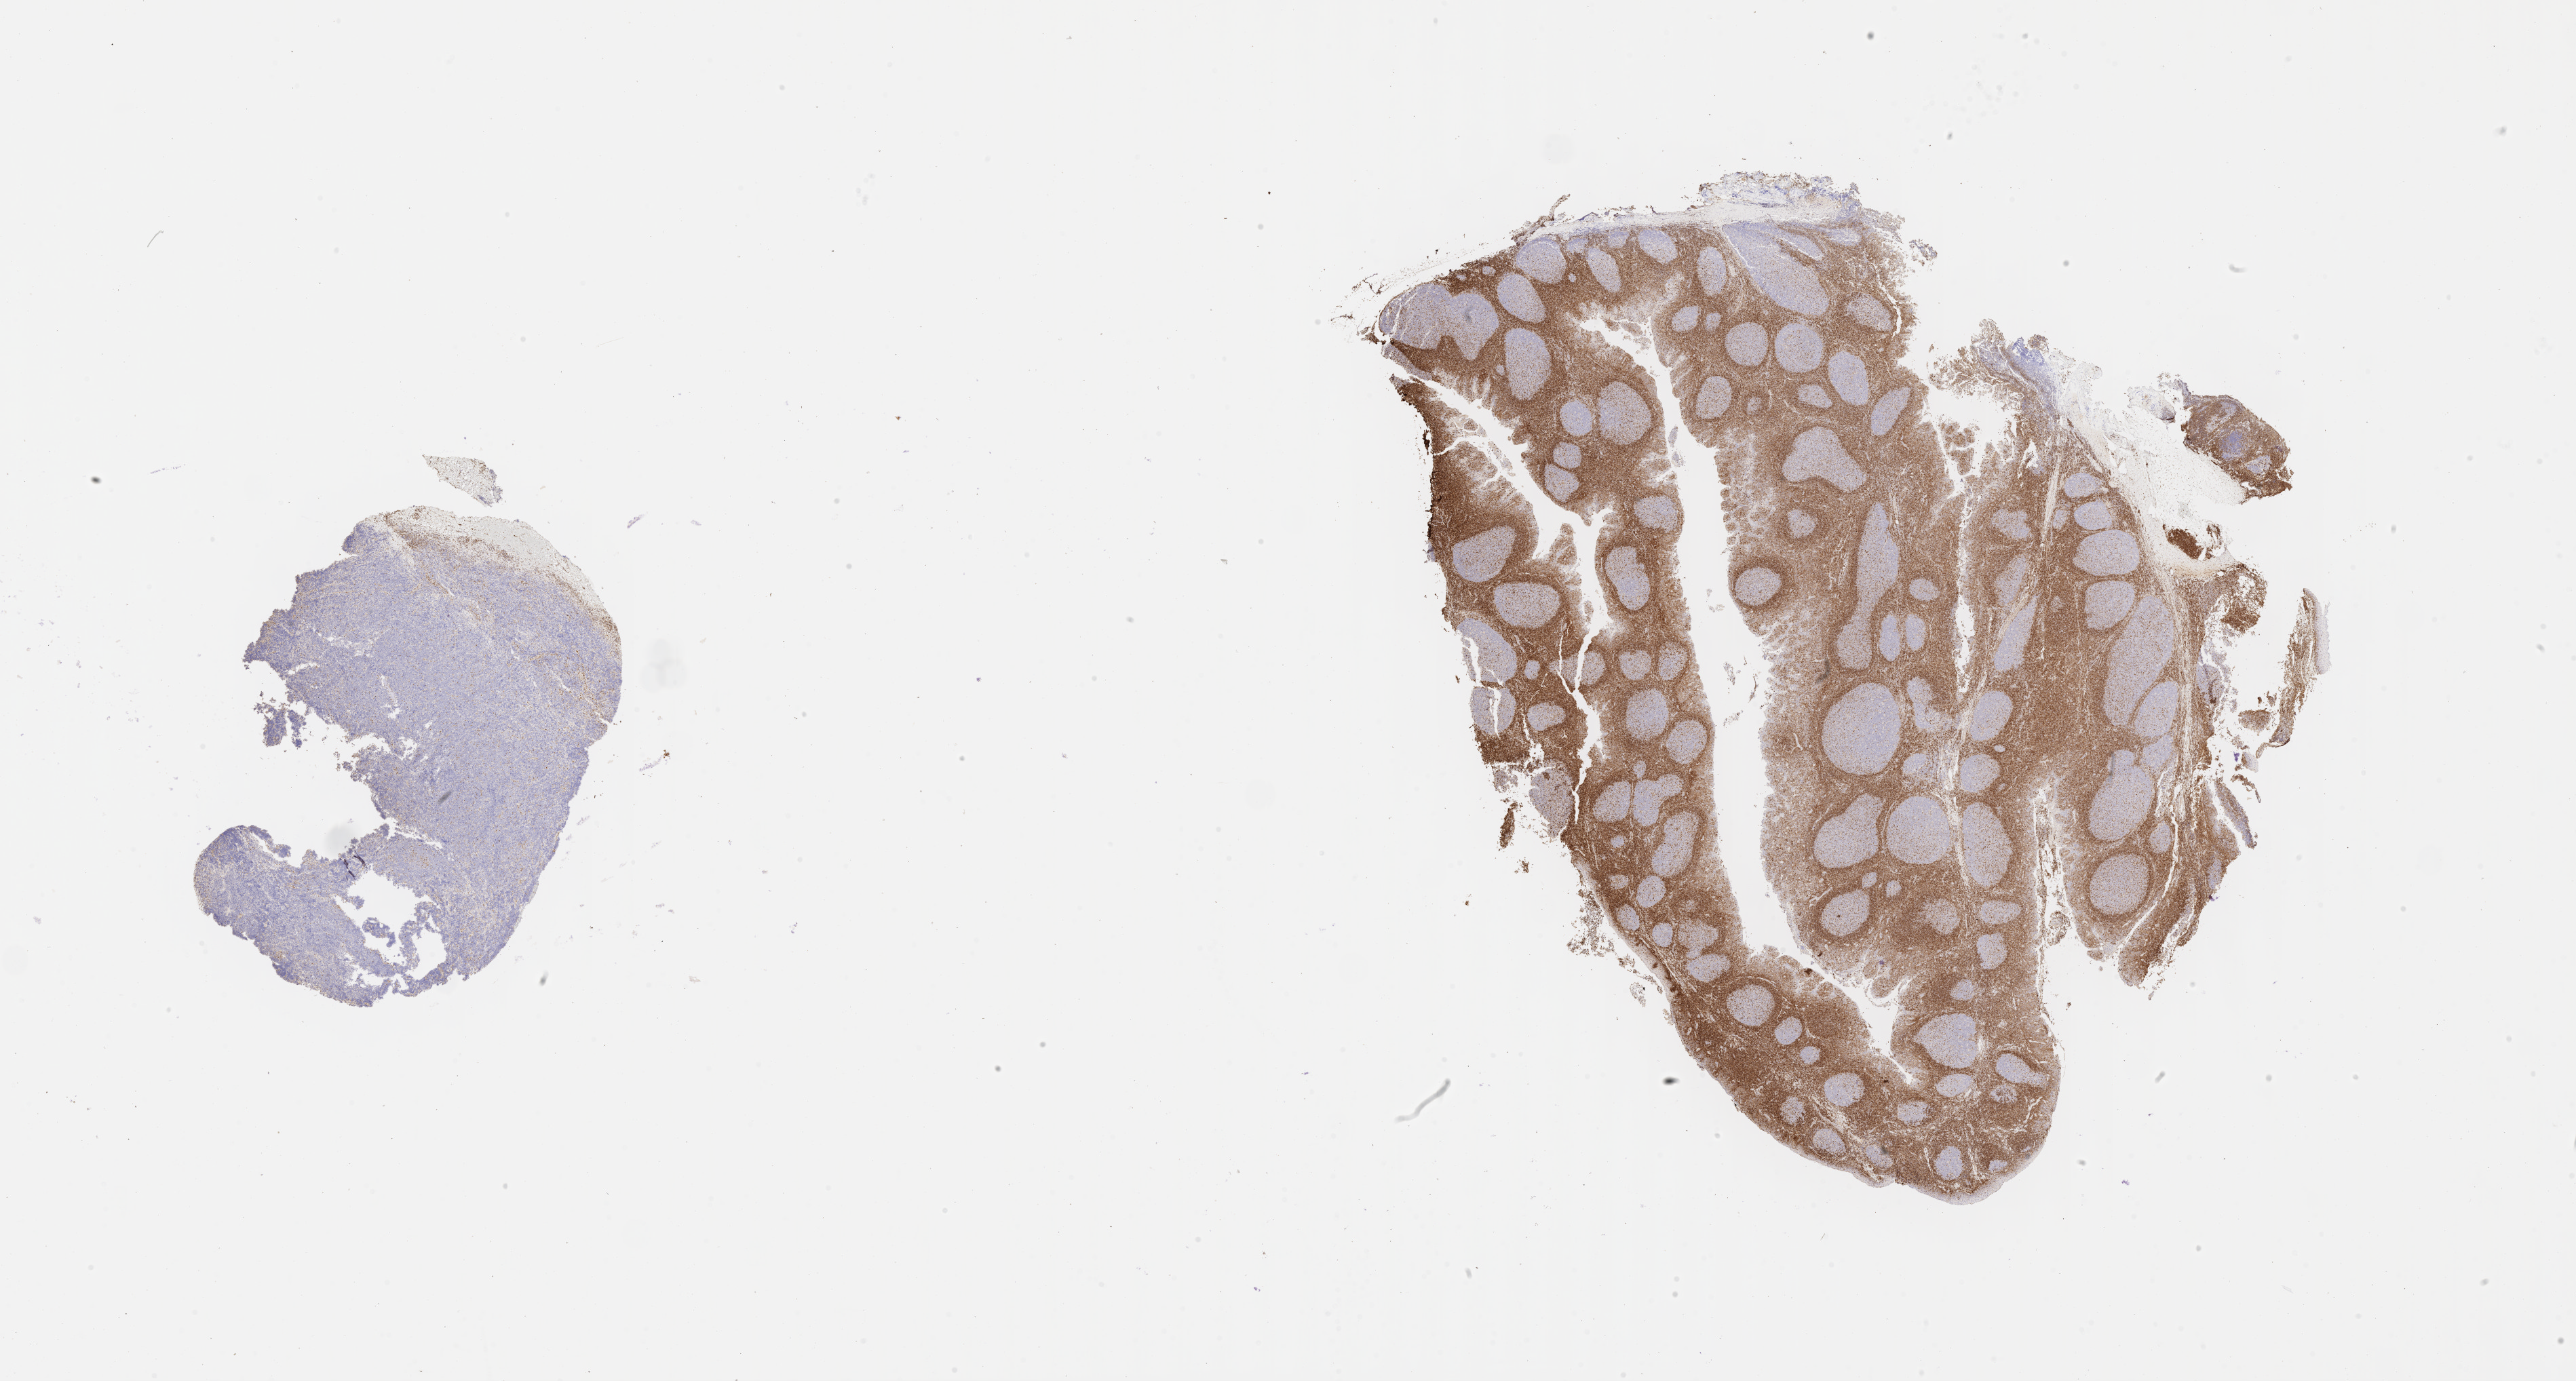
Whole-slide image, immunohistochemical stain for BCL2 — whole scanned area (about 30.7 x 16.5 mm) shown as a low-resolution overview. Tumor tissue. Anatomic site: mandible. Female patient; age at initial diagnosis 7 years.
Histologic diagnosis: Burkitt lymphoma, NOS.